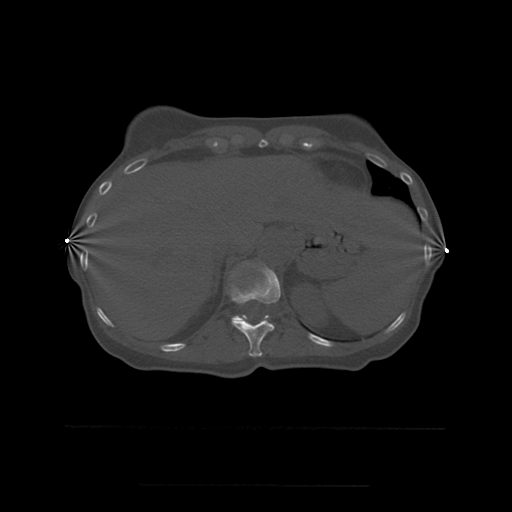
CT including the spine, one axial slice; slice 274 of 544 in the series (ordered by position); bone window (W 1800 / L 400 HU); 1.25 mm slice thickness; 512 × 512 image matrix, field of view 350 × 350 mm. Patient age 58 years. From the clinical record (not read from this slice): primary cancer: lung.
Annotated regions visible in this slice (semi-automatic segmentation, software-assisted and operator-edited):
- T11 vertebra: bounding box (x1, y1, x2, y2) in pixels: (231, 264, 281, 357)
- T12 vertebra: (231, 265, 276, 322)